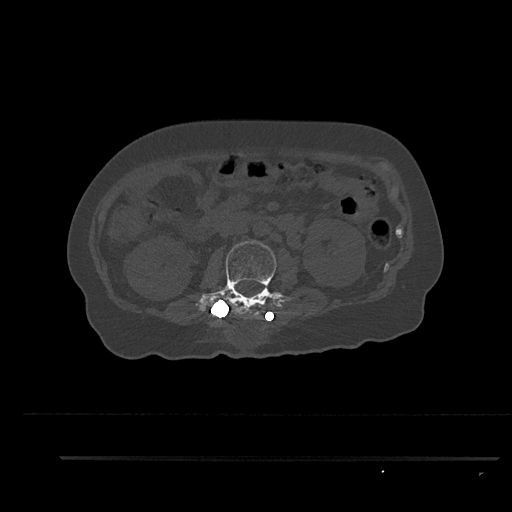
CT including the spine, one axial slice. Reconstruction kernel Br40s/3. Bone window (W 1800 / L 400 HU). 0.5 mm slice thickness. 512 × 512 image matrix. Patient: female, 44 years. Case-level facts recorded for this patient, not image findings: primary cancer: renal; vertebrae with lytic lesions (as recorded): L1.
Annotated regions visible in this slice (semi-automatic segmentation, software-assisted and operator-edited):
- L2 vertebra: bounding box (x1, y1, x2, y2) in pixels: (196, 240, 282, 318)